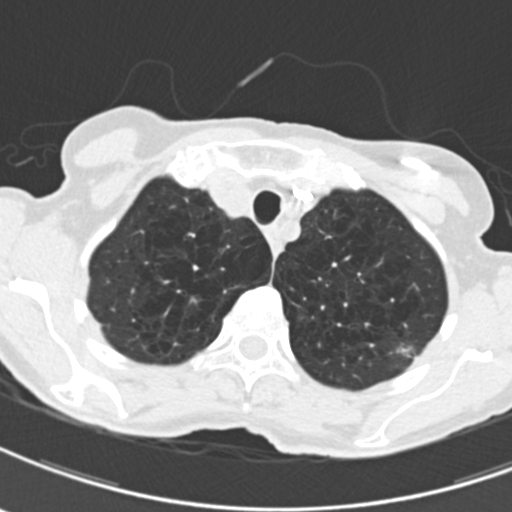
Low-dose screening chest CT, one axial slice; slice 168 of 203 in the series (ordered by position); lung window (W 1500 / L -600 HU); 2 mm slice thickness; 512 × 512 image matrix, field of view 279 × 279 mm.
Annotated regions visible in this slice (expert manual segmentation):
- lesion 1 (tumor, upper lobe of left lung): bounding box [x1, y1, x2, y2] px = [390, 342, 416, 358]